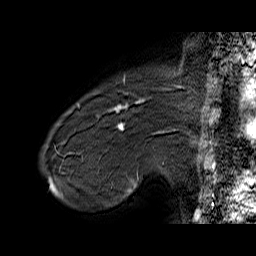
Breast MRI (dynamic contrast-enhanced), one sagittal slice; slice 11 of 60 in the series (ordered by position); dynamic contrast-enhanced series, time point 2 of 6 at this slice position (early post-contrast); 1.5 T; TE 6.4 ms, TR 32.9 ms; 256 × 256 image matrix, field of view 200 × 200 mm. Female patient. Case-level facts recorded for this patient, not image findings: setting: breast cancer imaged before/during neoadjuvant chemotherapy; receptor status: HER2-positive.
Annotated regions visible in this slice (semi-automatic segmentation, software-assisted and operator-edited):
- analysis volume of interest (the breast-tissue region the enhancement analysis was run in; not a lesion): box from (x=71, y=80) to (x=155, y=146) px
- tumour enhancement mask (voxels above the 100 % enhancement threshold inside the analysis volume of interest): (x=99, y=99)–(x=143, y=127)